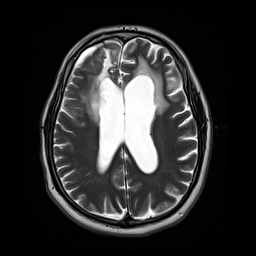
Brain MRI from a brain-tumour surgery series, one axial slice; position 17 of 44 along the scan axis; 4 mm slice thickness; 256 × 256 image matrix, field of view 240 × 240 mm. From the clinical record (not read from this slice): histopathology: Astrocytoma; WHO grade: 4; IDH mutation: yes; tumour location: Right Frontal.
Annotated regions visible in this slice (manually delineated by an expert):
- tumour: bounding box <87,94,101,125> (left, top, right, bottom; pixels)